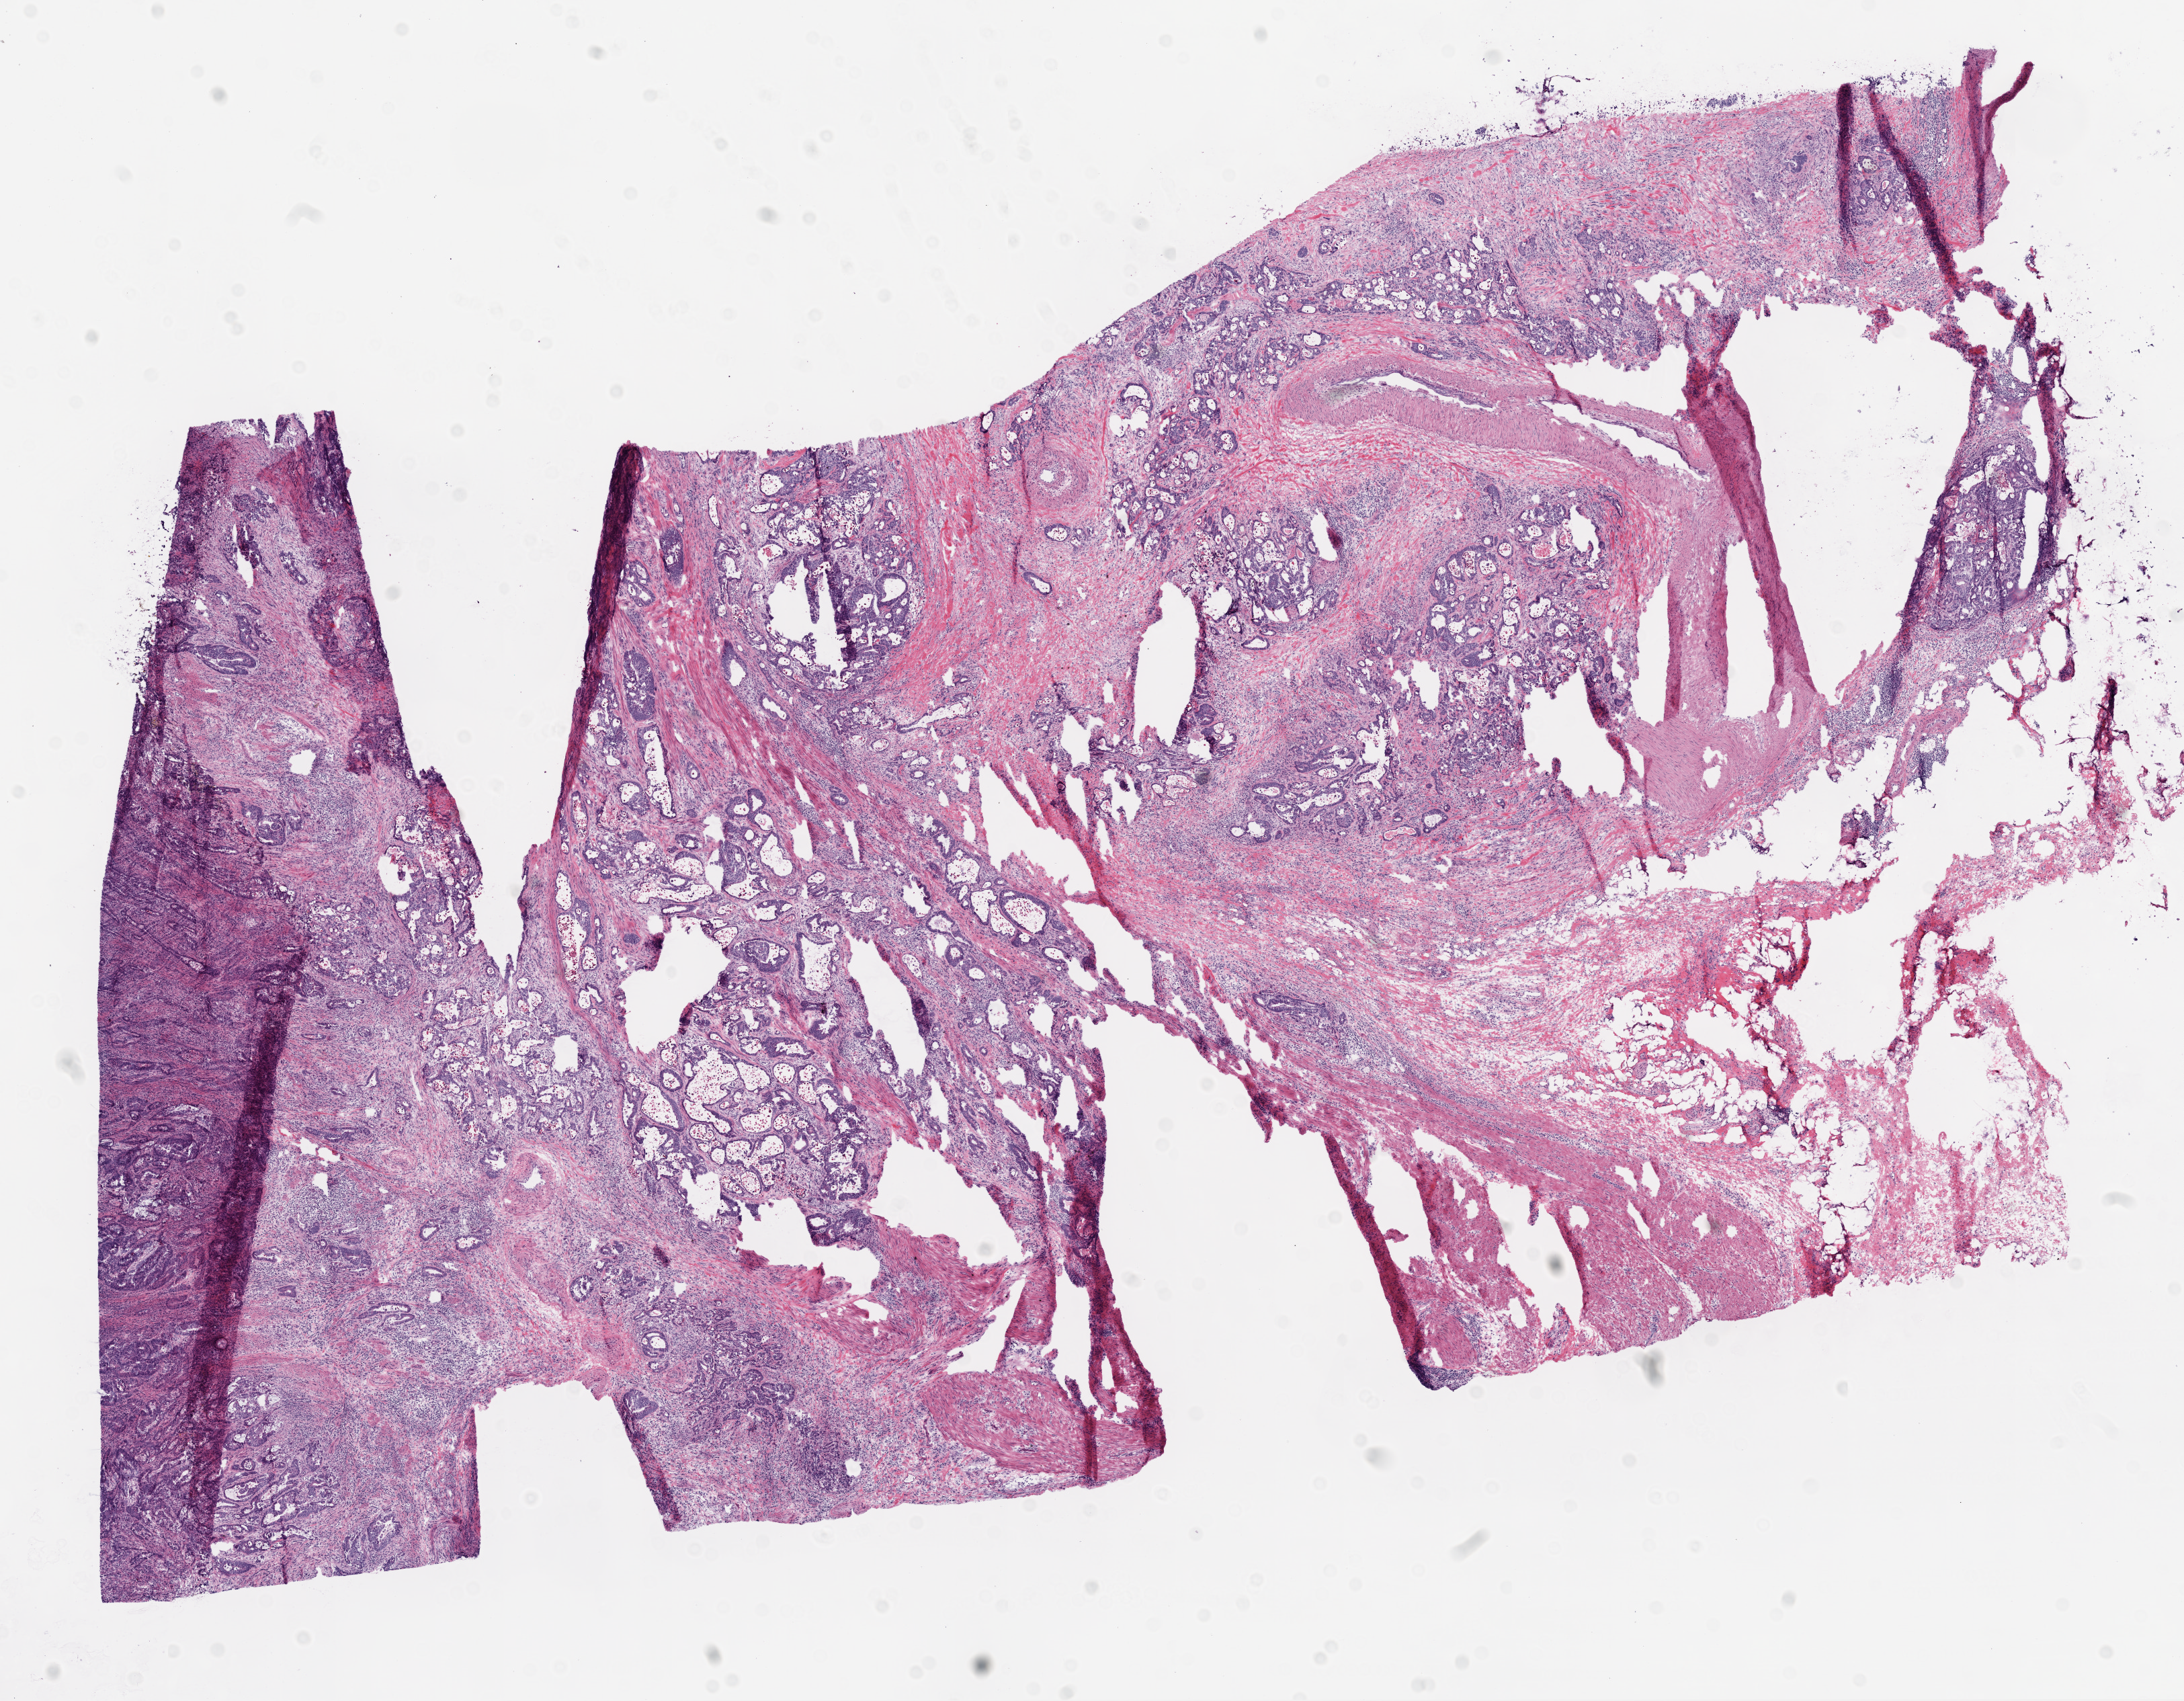
Digitized H&E tissue section (whole slide), shown as a low-resolution overview of the whole scanned area (about 13.0 x 10.2 mm, acquisition: 20x scan), frozen section, primary tumour sample from the rectum. Female patient; age at initial diagnosis 76 years. Composition of this section per pathologist review: tumour cells 60%, tumour nuclei 70%, normal cells 30%, stromal cells 10%, necrosis 0%.
- pathologic diagnosis: Adenocarcinoma, NOS
- AJCC pathologic stage: IIIC (6th edition)